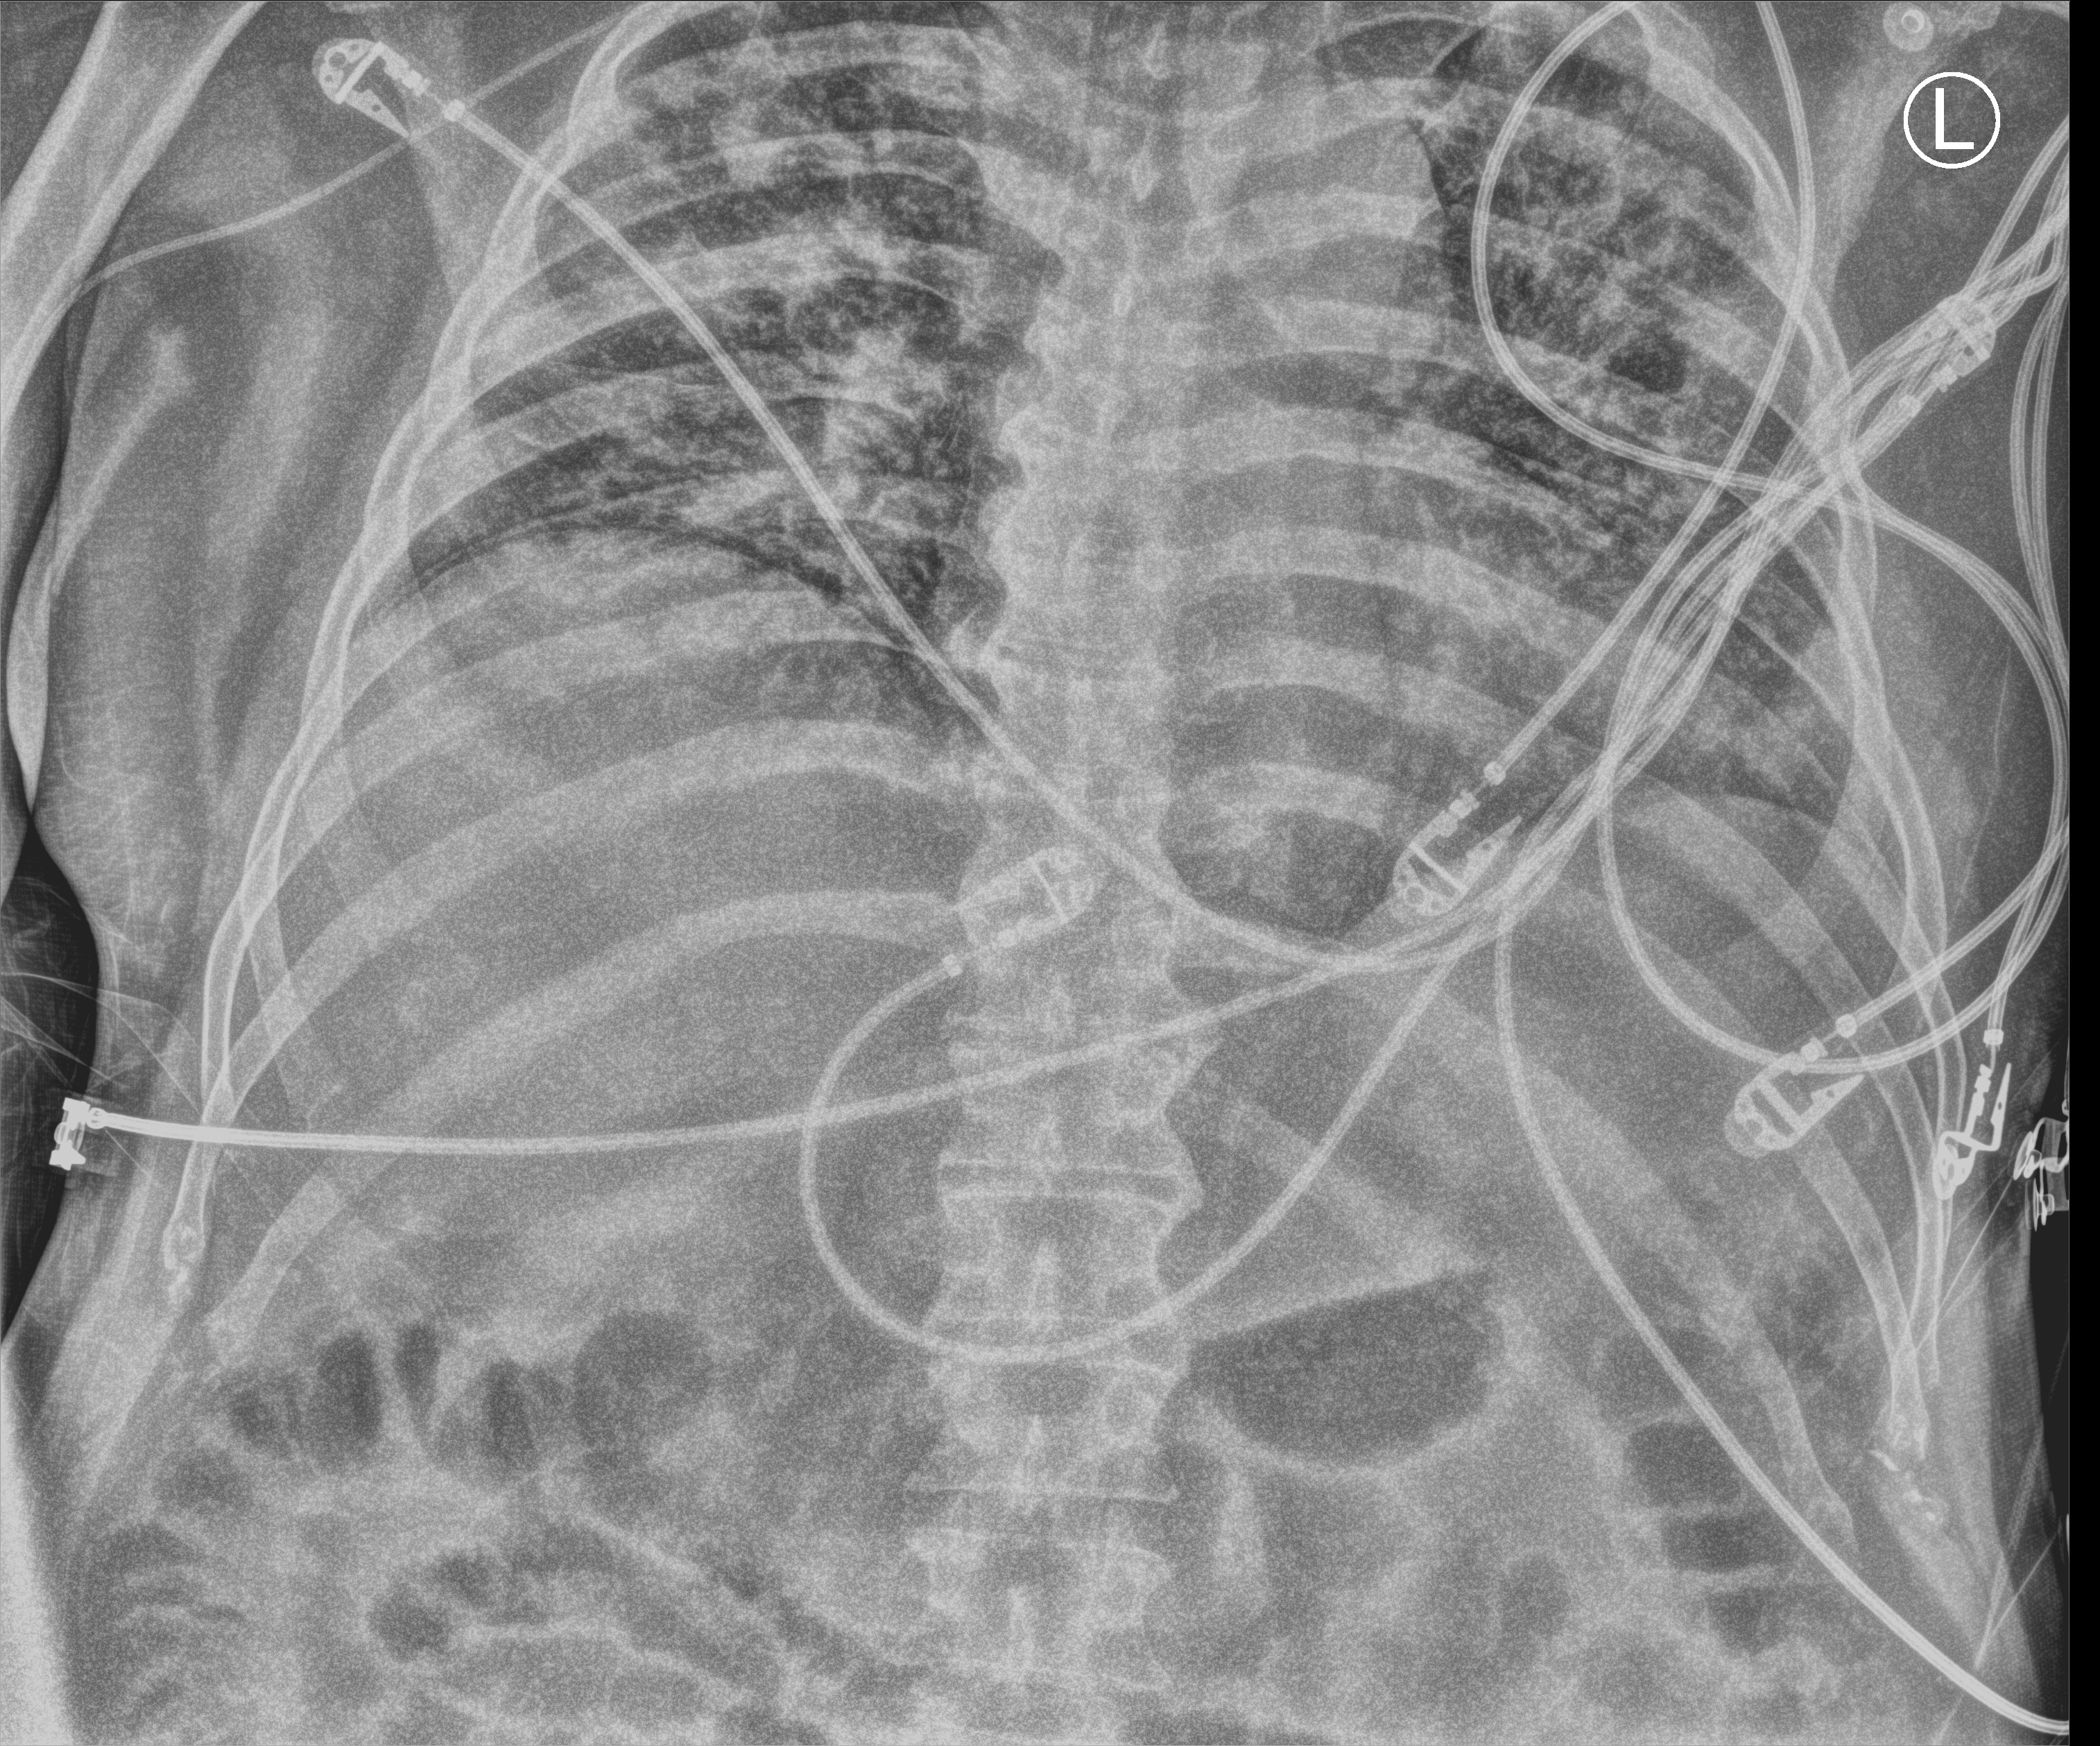
Chest X-ray (portable); anteroposterior (AP) projection. Patient hospitalised with COVID-19; male, aged 18–59 years.
Hospital-stay facts (about this admission, not read from this image; timing relative to this image not recorded): admitted to intensive care during this hospital stay: yes; mechanically ventilated during this hospital stay: yes.